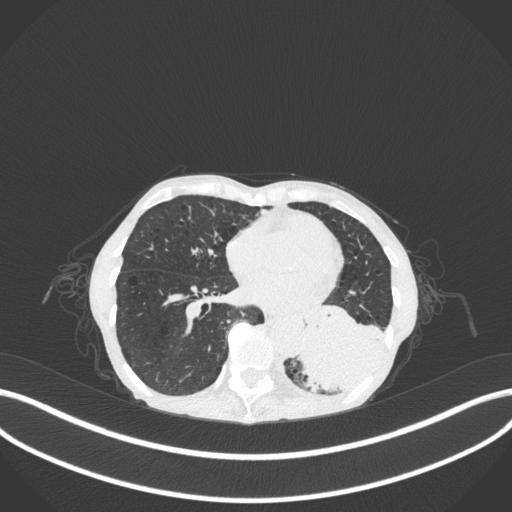
Chest CT, one axial slice; slice 100 of 347 in the series (ordered by position); reconstruction kernel B31f; 120 kVp; lung window (W 1500 / L -600 HU); 1 mm slice thickness; 512 × 512 image matrix, field of view 400 × 400 mm. Patient: female, 70 years. From the clinical record (not read from this slice): clinical TNM (as recorded): T3 N0 M0; histopathological grade: G3.
Outlined on this slice (bounding box drawn by a radiologist):
- lung tumour (recorded histology: small cell carcinoma): bounding box (x1, y1, x2, y2) in pixels: (295, 295, 390, 394)